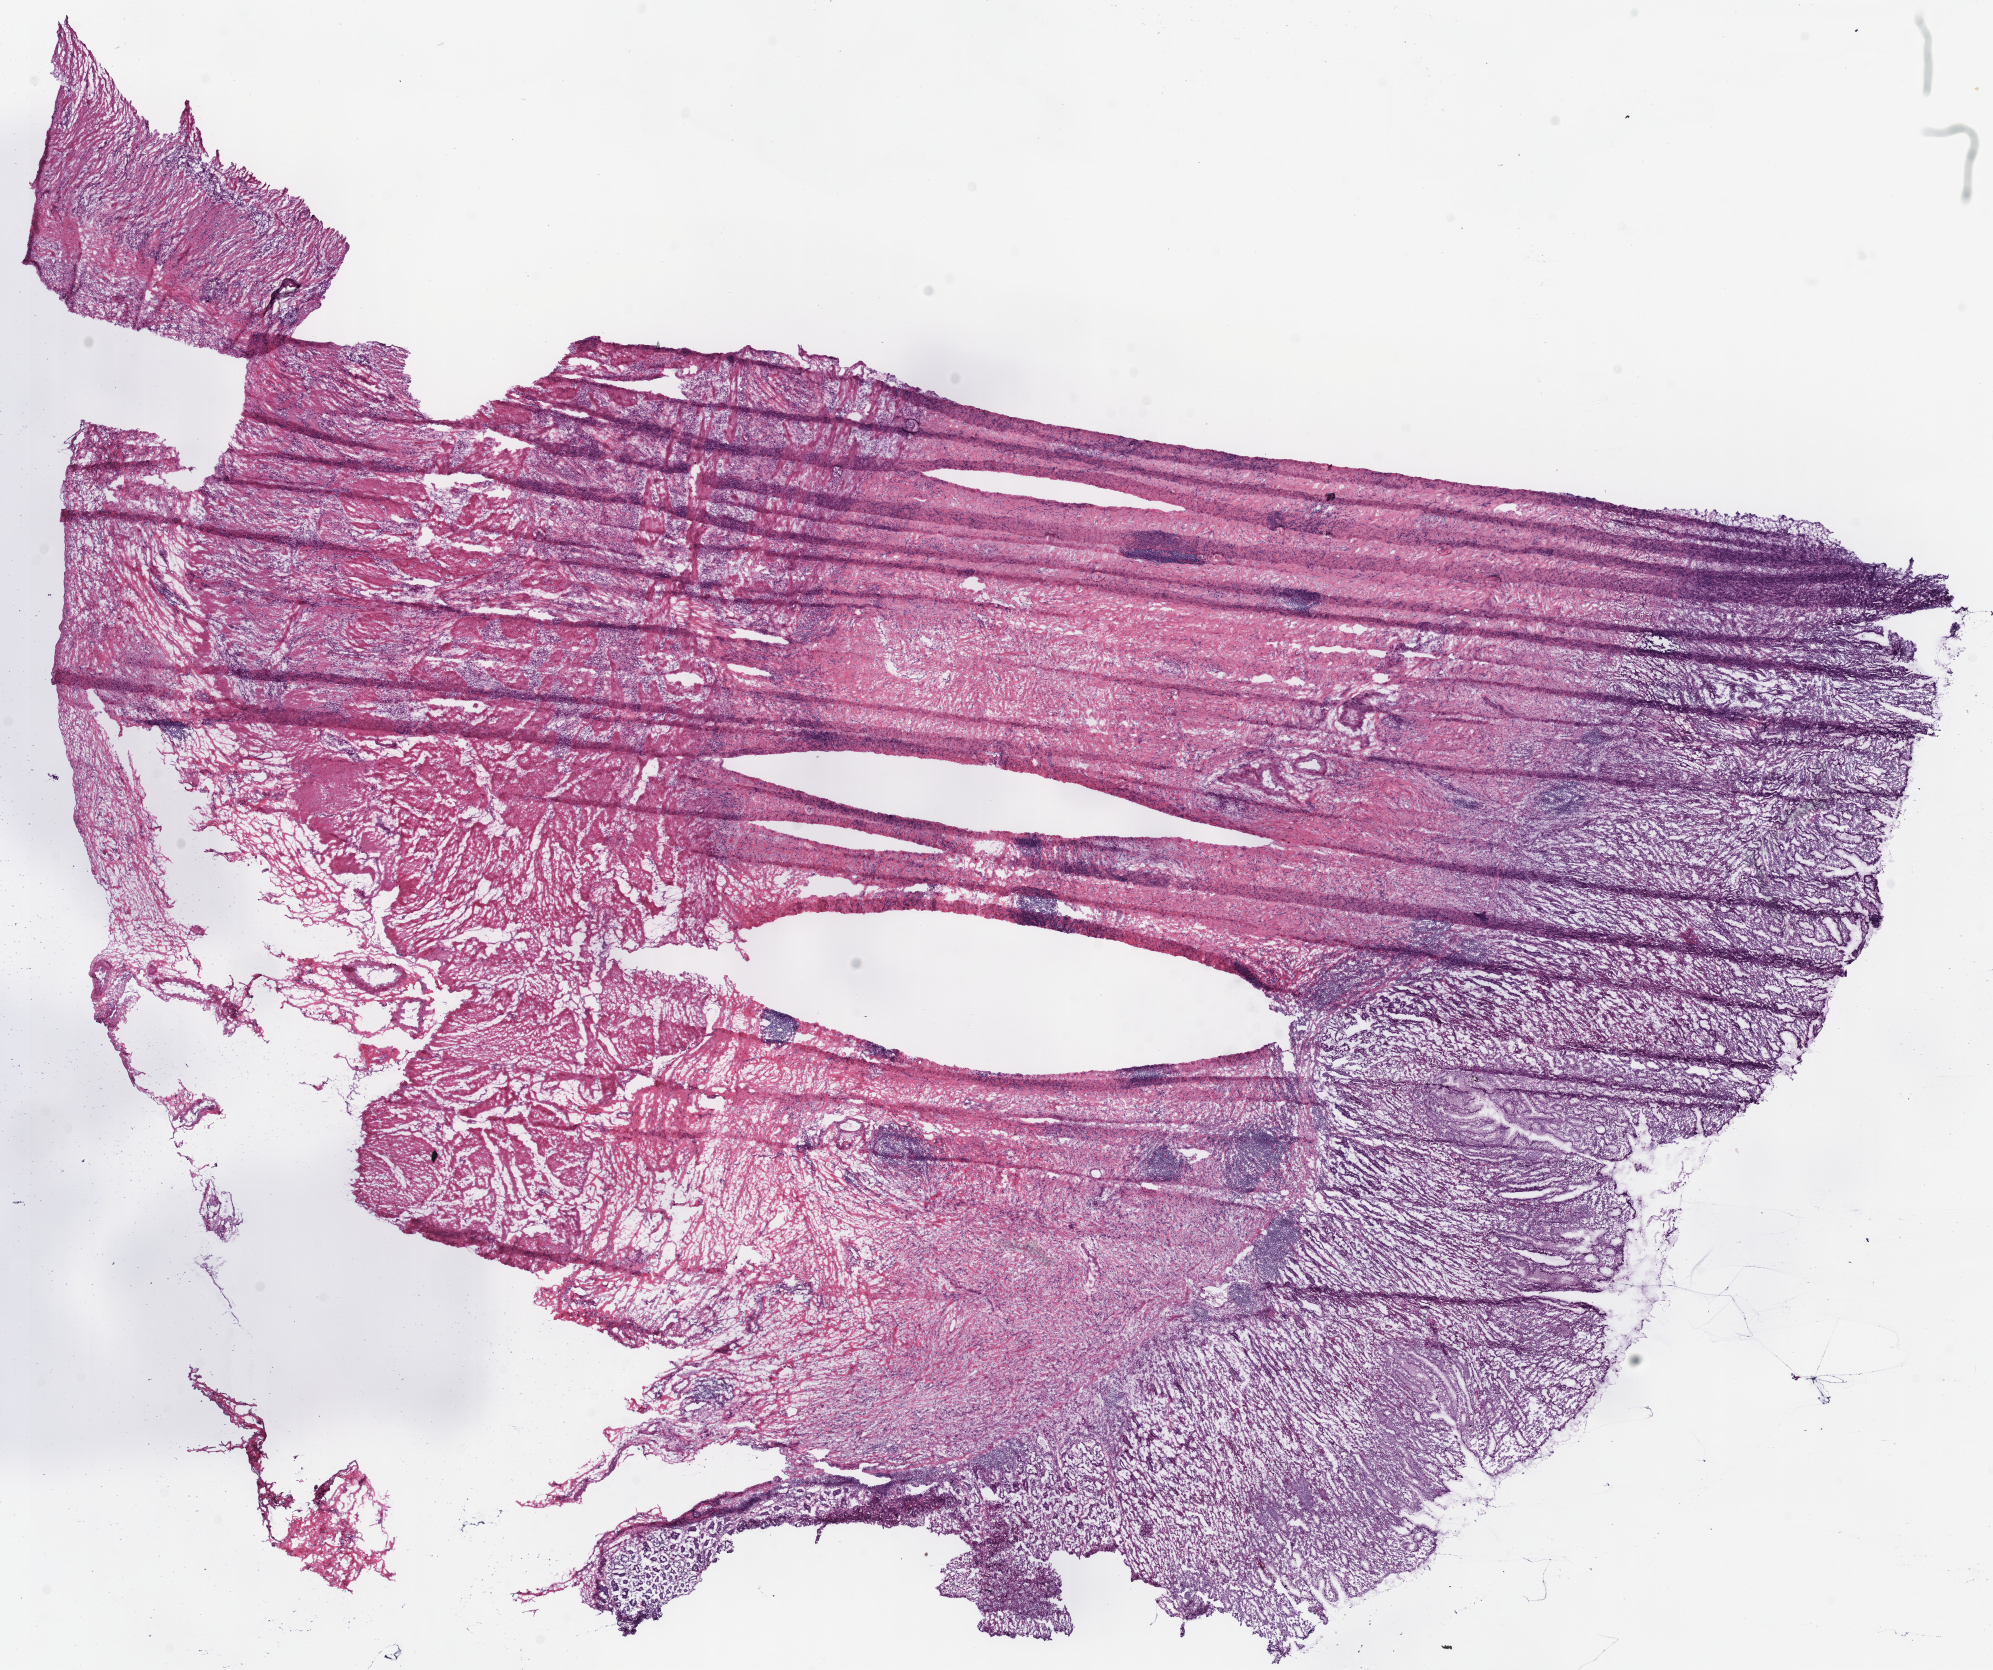
Whole-slide histology image, H&E — a low-resolution overview of the entire scanned area, about 15.7 x 13.2 mm; frozen section from the bottom of the tissue portion; sample: primary tumour, stomach. Patient: female, age at initial diagnosis 42 years. Histologic grade: G3 (poorly differentiated). Slide review estimates, as recorded: tumour cells 50%, tumour nuclei 50%, normal cells 10%, stromal cells 40%, necrosis 0%.
• histologic diagnosis: Carcinoma, diffuse type (fundus of stomach)
• lymph nodes positive (case pathology): 3 of 11 examined
• AJCC pathologic stage: IIIC (7th edition)